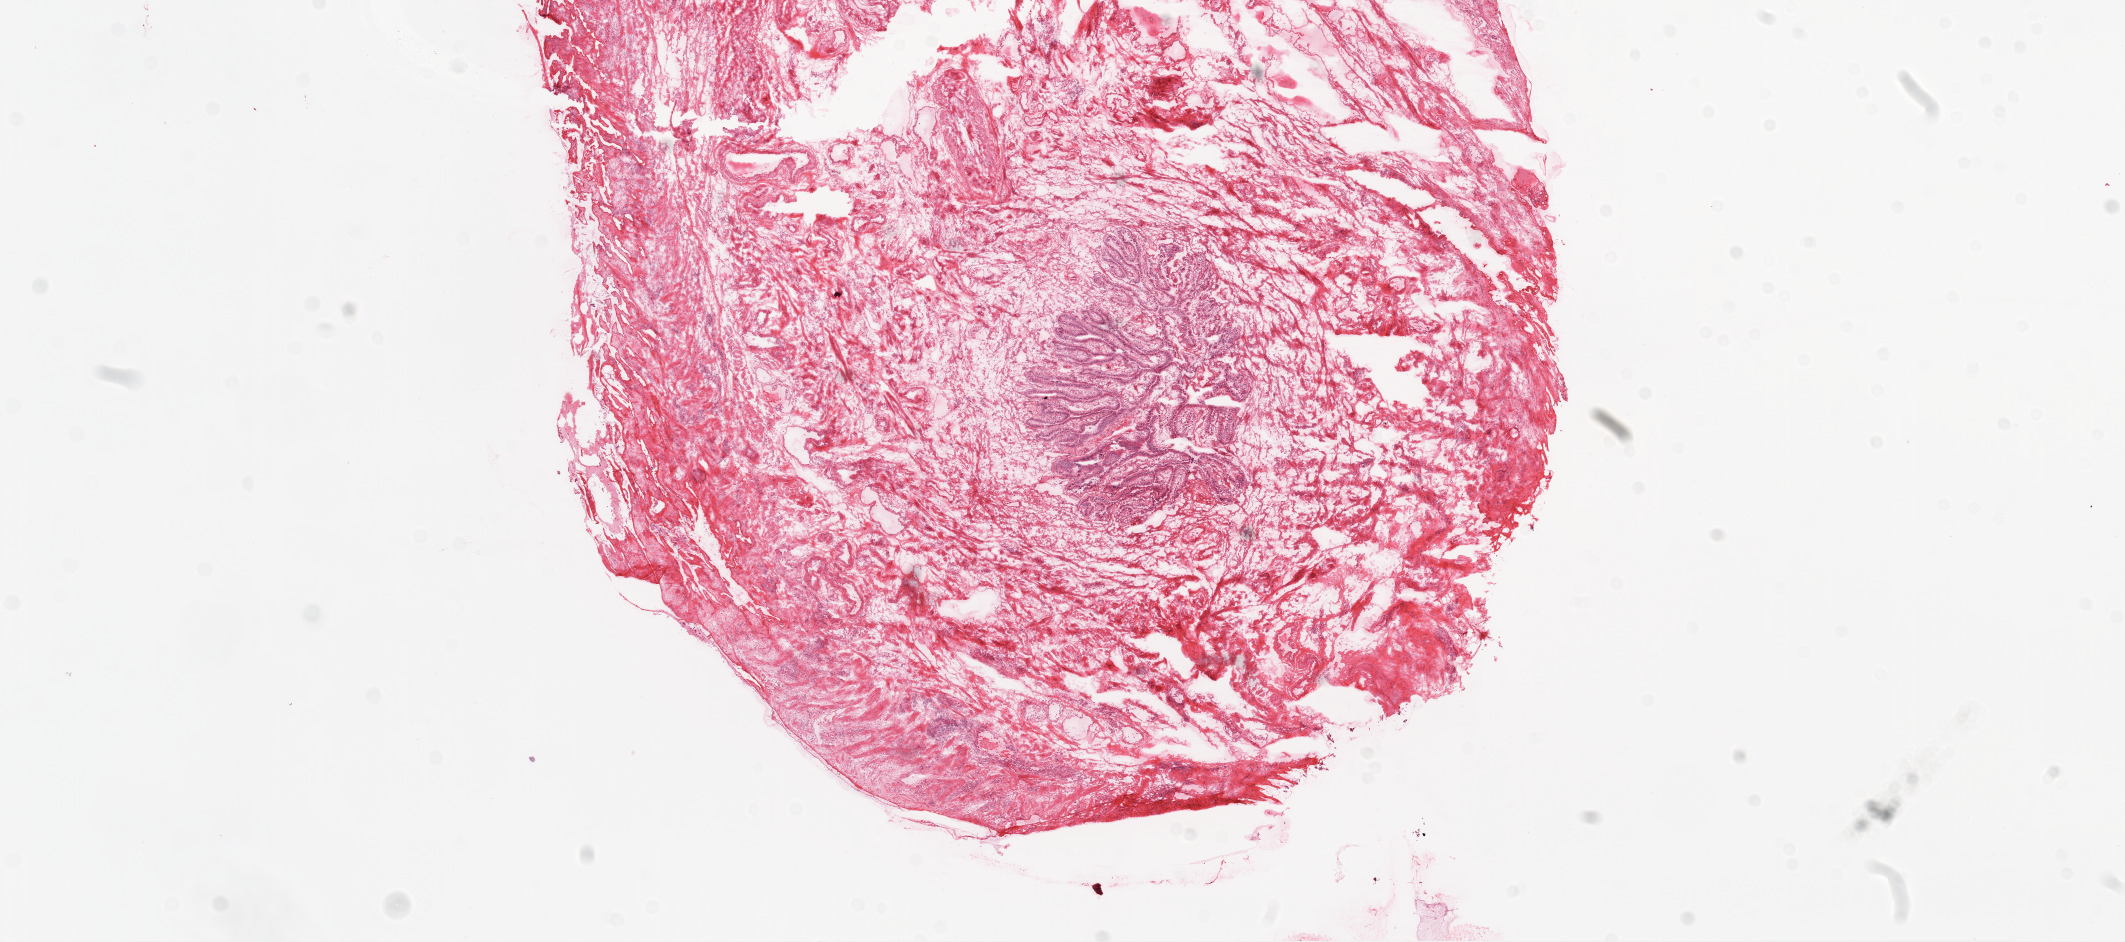
Hematoxylin and eosin (H&E) stained whole-slide image — shown as a low-resolution overview of the whole scanned area (about 17.1 x 7.6 mm, slide scanned at 20x). Frozen section from the top of the tissue portion. Ovary, solid tissue normal (non-tumour tissue) sample. Female patient; age at initial diagnosis 49 years.
This section: solid tissue normal (non-tumour) sample from the same patient. Patient diagnosis: Serous cystadenocarcinoma, NOS.